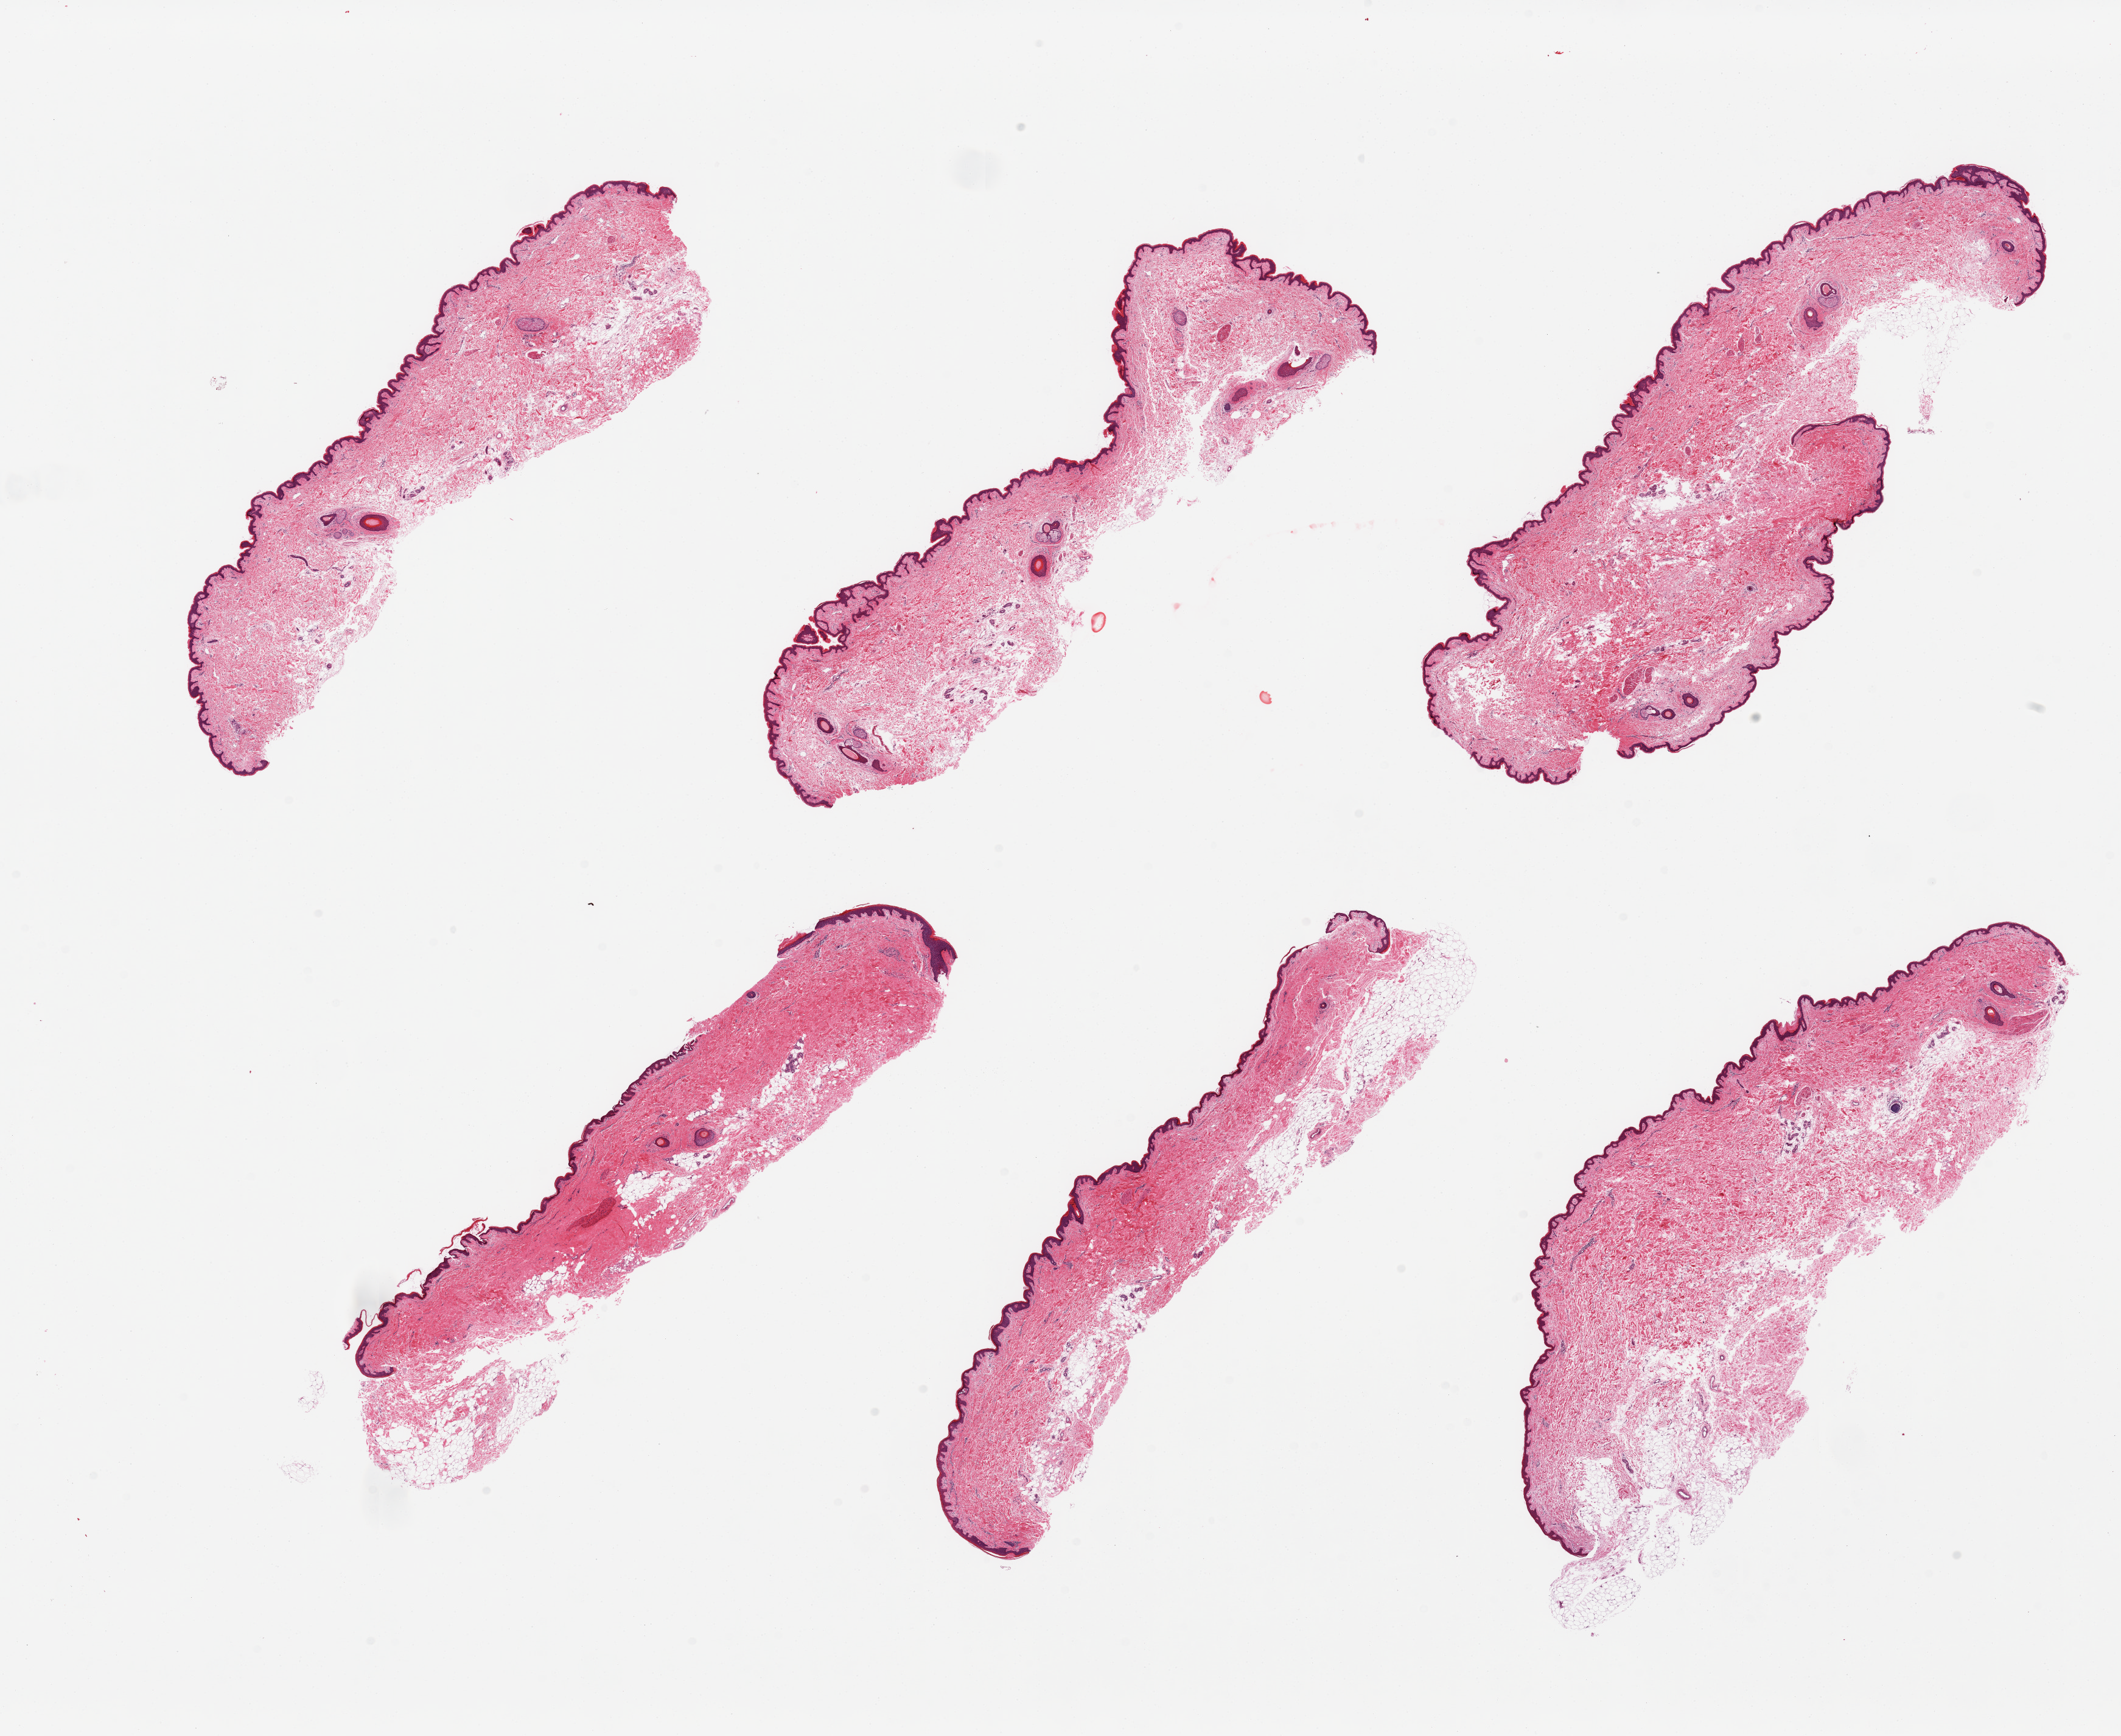
Hematoxylin and eosin (H&E) whole-slide image — low-resolution overview of the scanned area, about 27.6 x 22.6 mm (from a 20x scan). PAXgene-fixed, paraffin-embedded tissue. Sampled site (target tissue): skin of suprapubic region. Tissue donor sample. Female donor.
* pathologist's review note for this sample: 6 pieces of skin